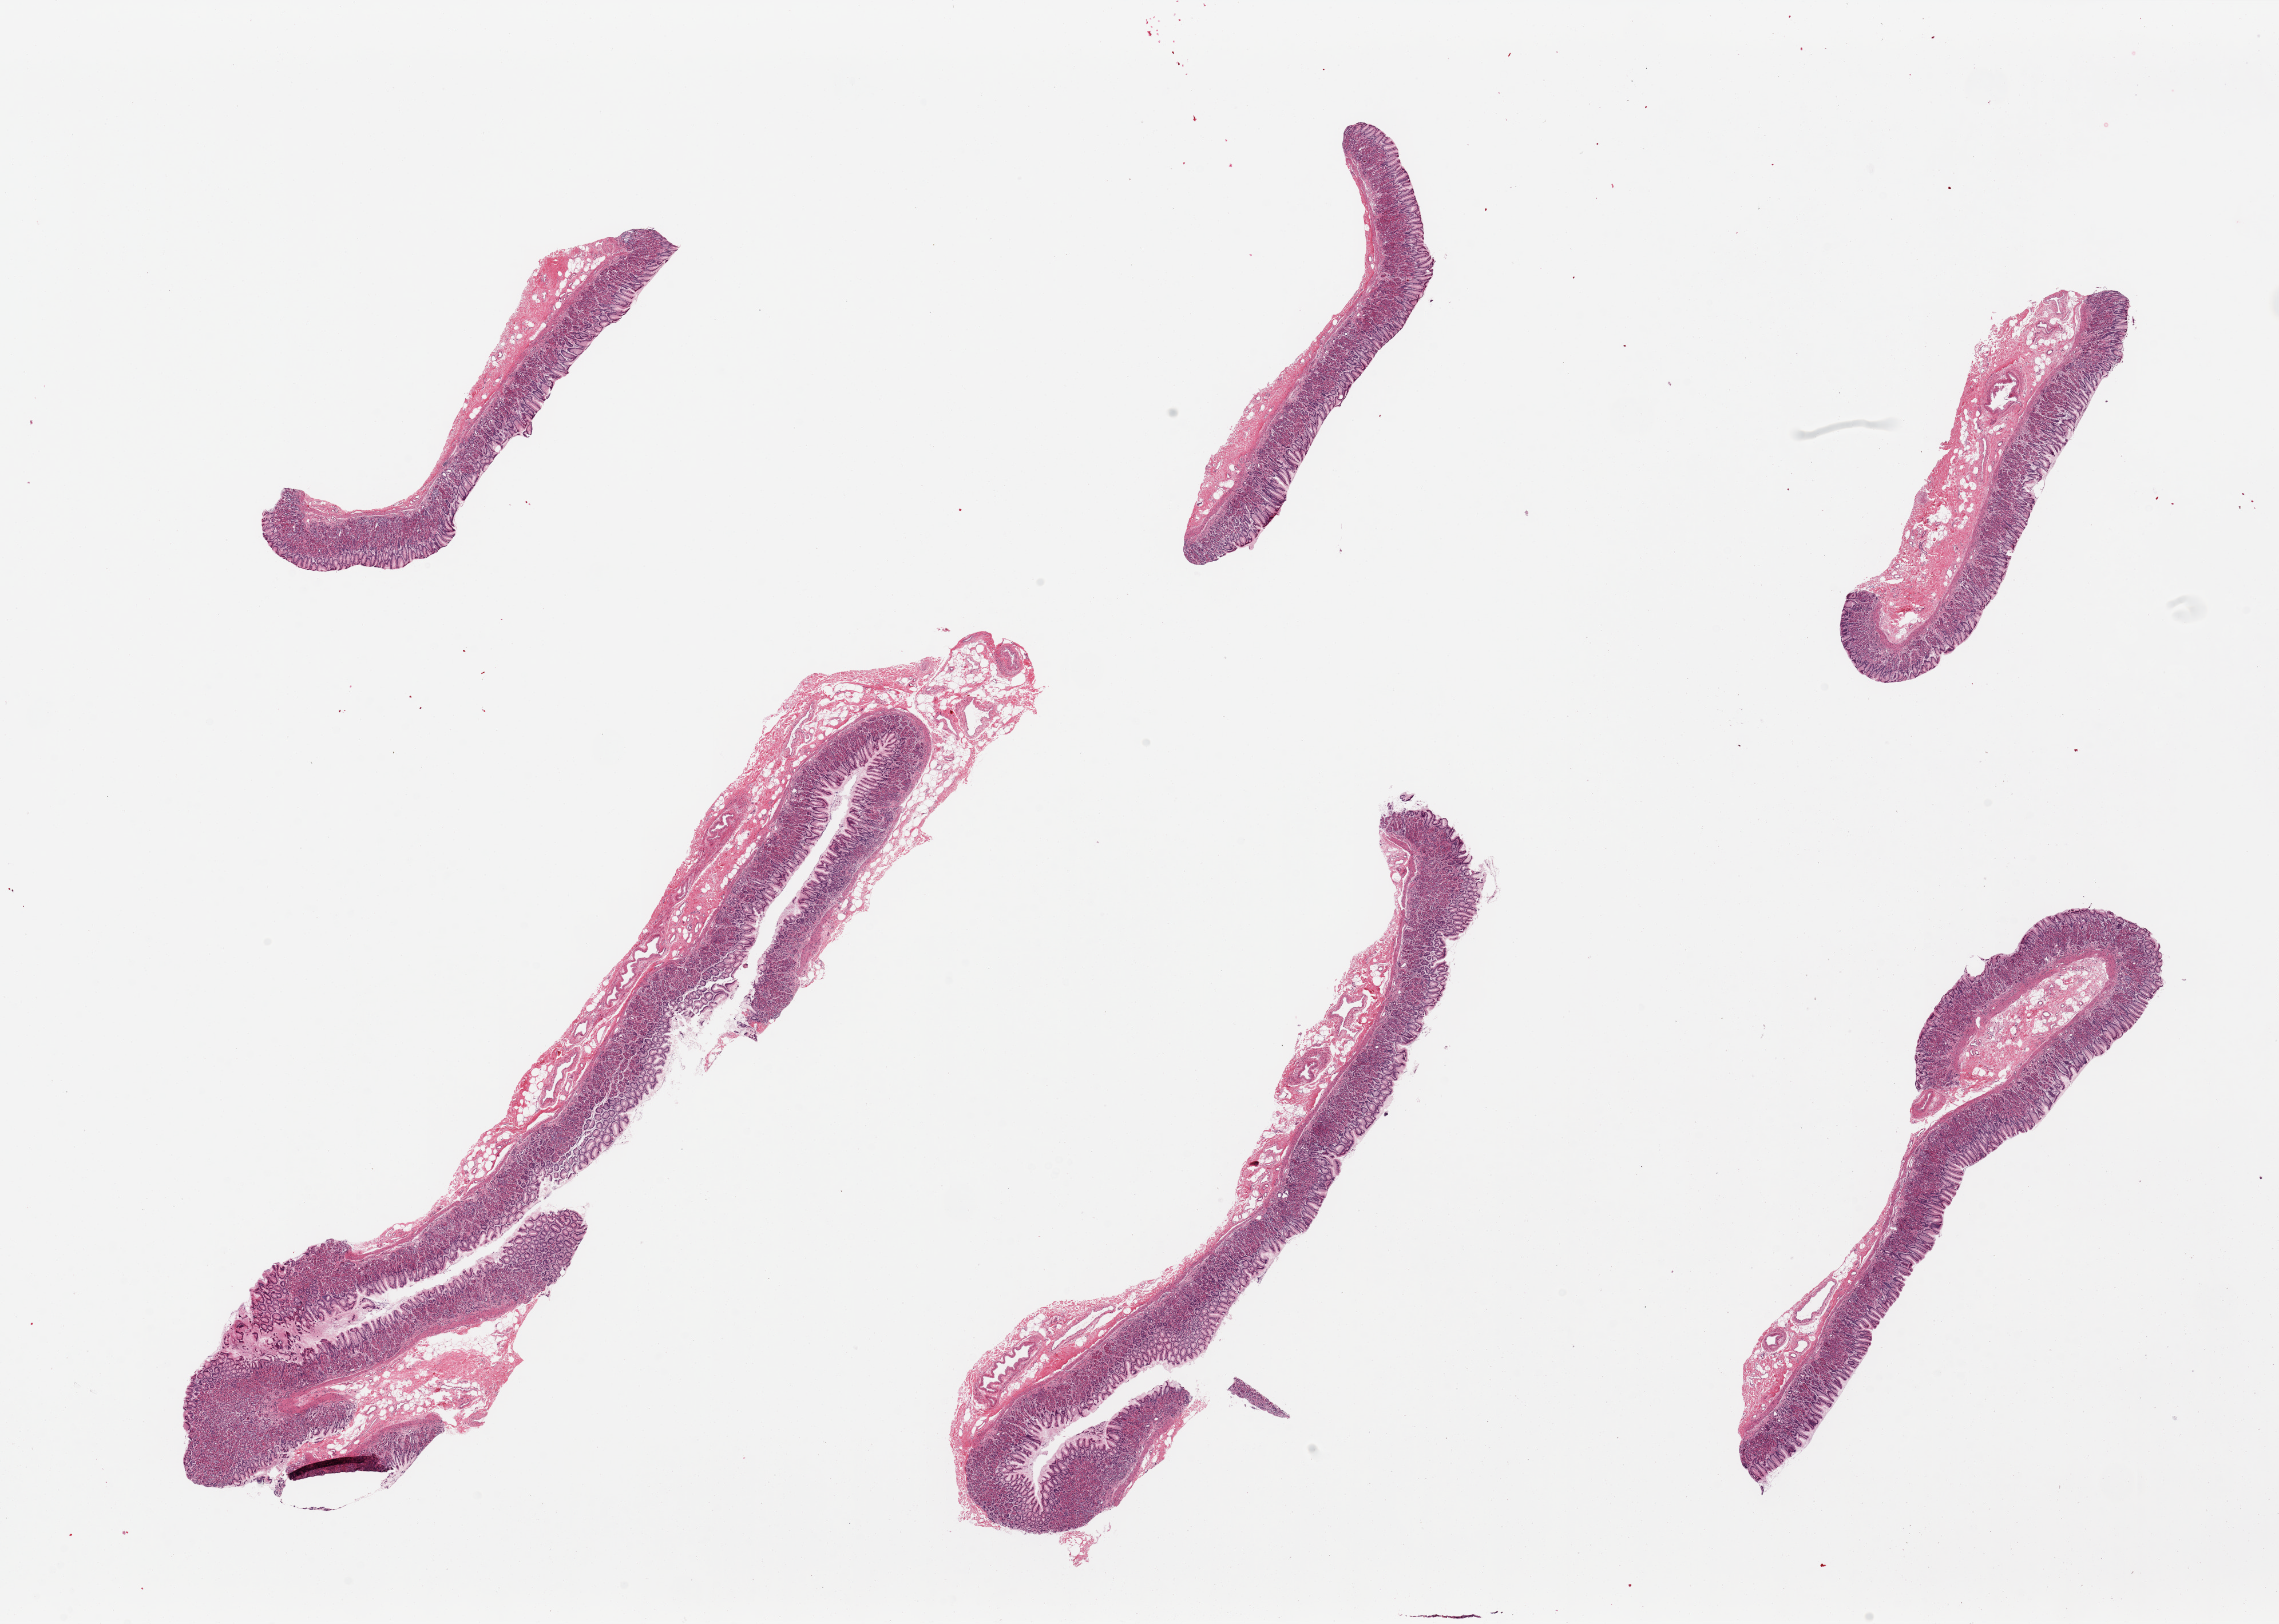
Digitized haematoxylin and eosin-stained section, brightfield — low-resolution overview of the scanned area, about 31.5 x 22.5 mm; PAXgene-fixed paraffin-embedded (PFPE) section; target tissue: stomach; donor tissue sample. Donor: female.
• review note (as recorded): 6 pieces. Mucosa only present